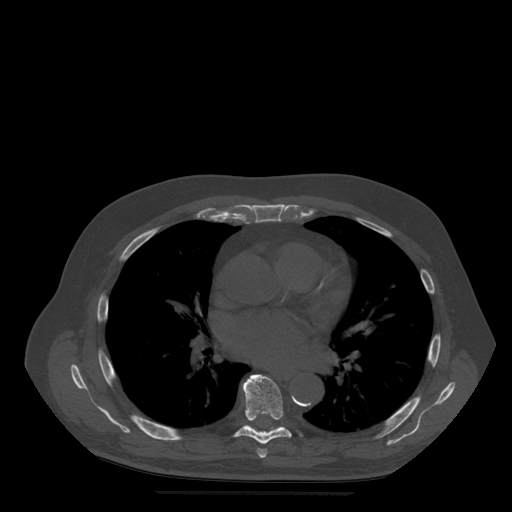
CT including the spine, one axial slice; position 333 of 522 along the scan axis; bone window (W 1800 / L 400 HU); 1.25 mm slice thickness; 512 × 512 image matrix, field of view 420 × 420 mm. Patient age 72 years. Case-level facts recorded for this patient, not image findings: primary cancer: prostate.
Structures marked on this image (semi-automatically segmented with operator editing):
- T6 vertebra: bounding box (x1, y1, x2, y2) in pixels: (257, 449, 268, 459)
- T7 vertebra: (233, 375, 292, 445)
- T8 vertebra: (248, 426, 284, 430)